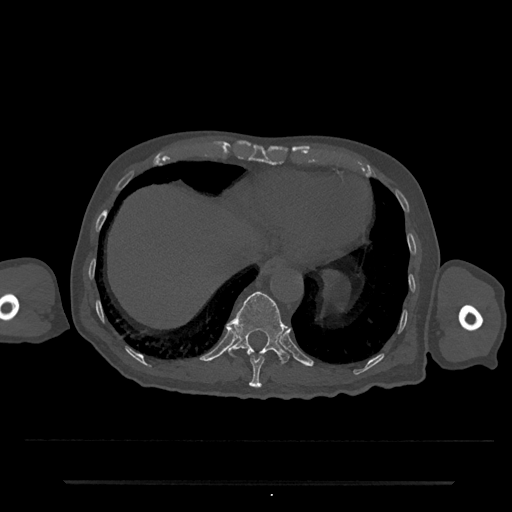
CT including the spine, one axial slice. Slice 276 of 797 in the series (ordered by position). Reconstruction kernel Br40s/3. 120 kVp. Bone window (W 1800 / L 400 HU). 0.5 mm slice thickness. 512 × 512 image matrix, field of view 427 × 427 mm. Male patient, age 74 years. Case-level facts recorded for this patient, not image findings: primary cancer: prostate.
Outlined on this slice (semi-automatic segmentation, software-assisted and operator-edited):
- T10 vertebra: bounding box <249,355,265,388> (left, top, right, bottom; pixels)
- T11 vertebra: <228,292,289,363>